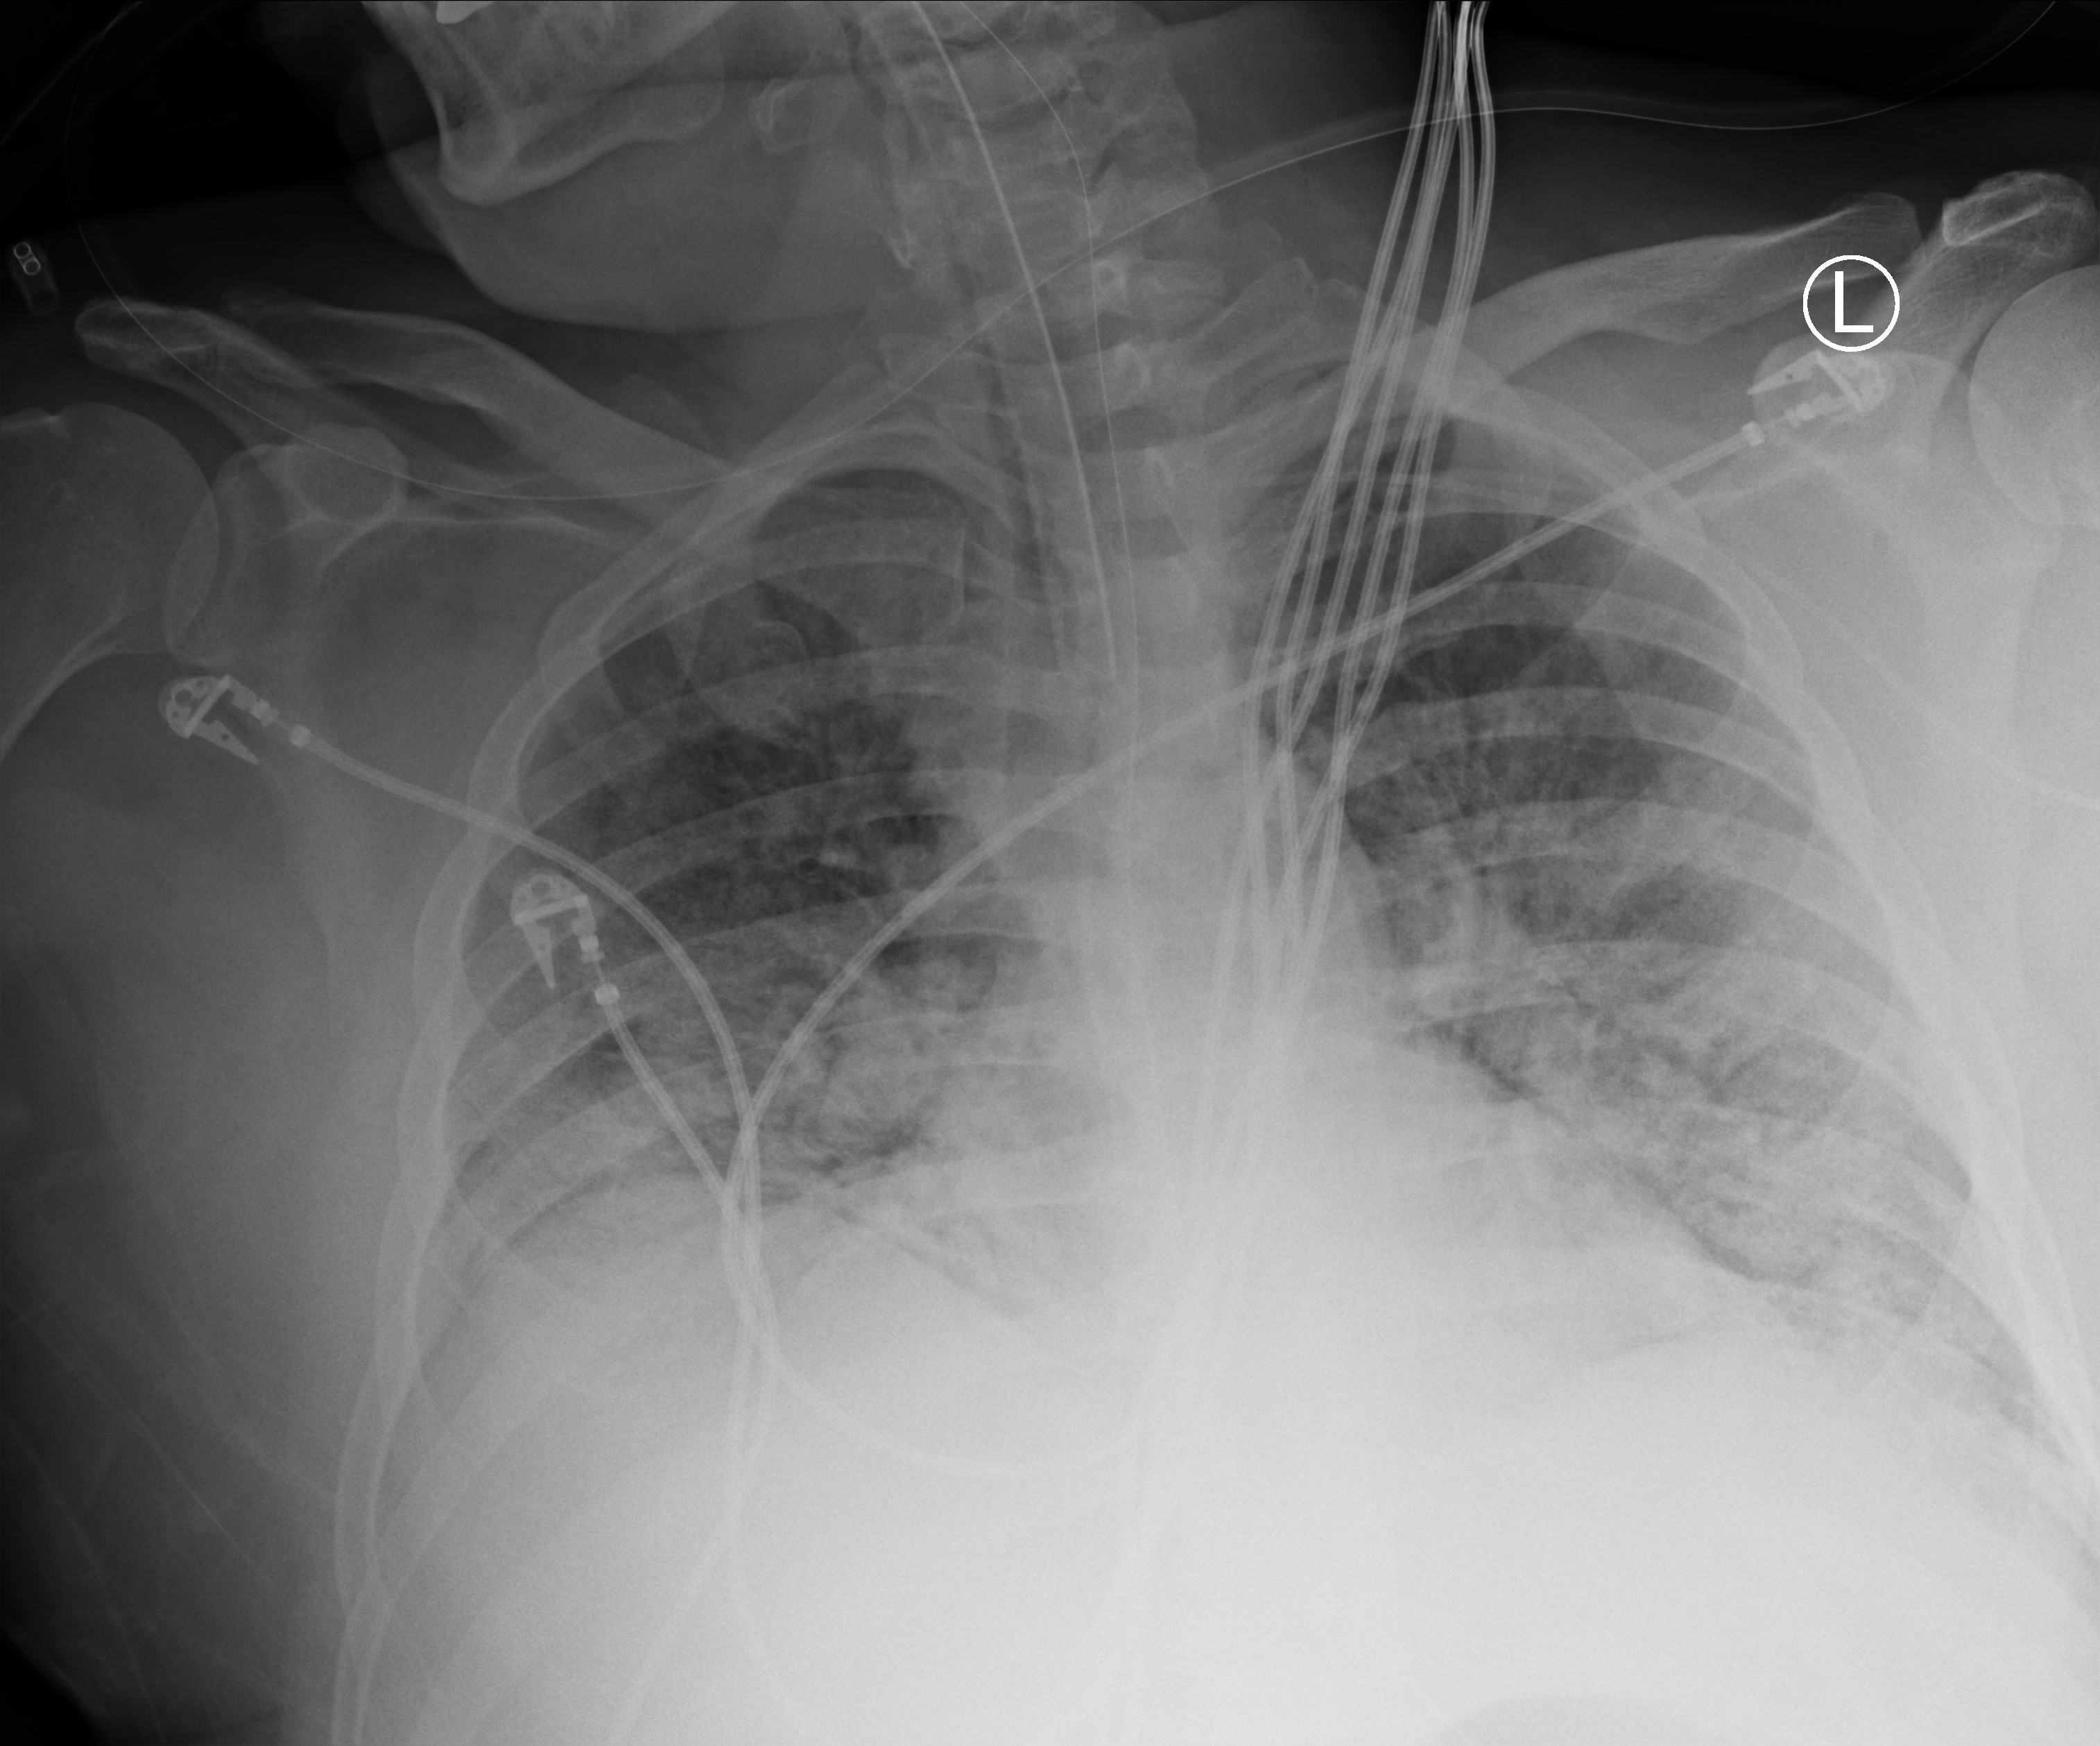
Bedside chest radiograph (computed radiography), anteroposterior (AP) projection. Male patient hospitalised with COVID-19, age 18–59 years.
From the hospital-stay record, not from the radiograph (when in the stay this image was taken is not recorded): mechanically ventilated during this hospital stay: yes; length of hospital stay: 80 days; admitted to intensive care during this hospital stay: yes.